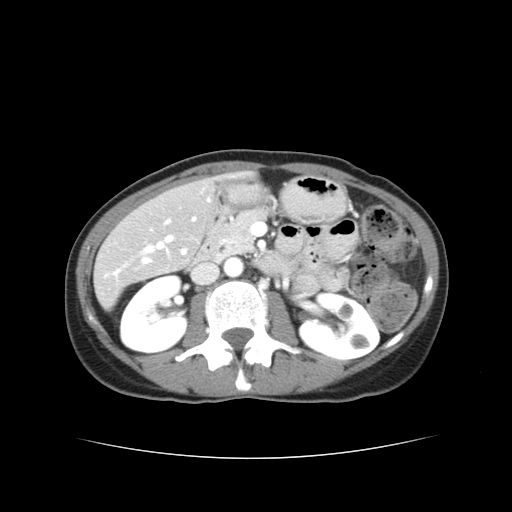
Contrast-enhanced abdominal CT, one axial slice; slice 15 of 38 in the series (ordered by position); reconstruction kernel STANDARD; soft-tissue window (W 400 / L 40 HU); 5 mm slice thickness; 512 × 512 image matrix, field of view 340 × 340 mm. Female patient, age 54 years. From the clinical record (not read from this slice): diagnosis: colorectal cancer liver metastases, imaged before liver resection; multiple liver metastases: yes; largest metastasis: 1.1 cm; disease in both lobes: yes.
Outlined on this slice (outlined manually by an expert reader):
- hepatic veins: box from (x=144, y=236) to (x=173, y=253) px
- liver: (x=95, y=179)–(x=215, y=304)
- portal vein (with intrahepatic branches): (x=143, y=218)–(x=196, y=263)